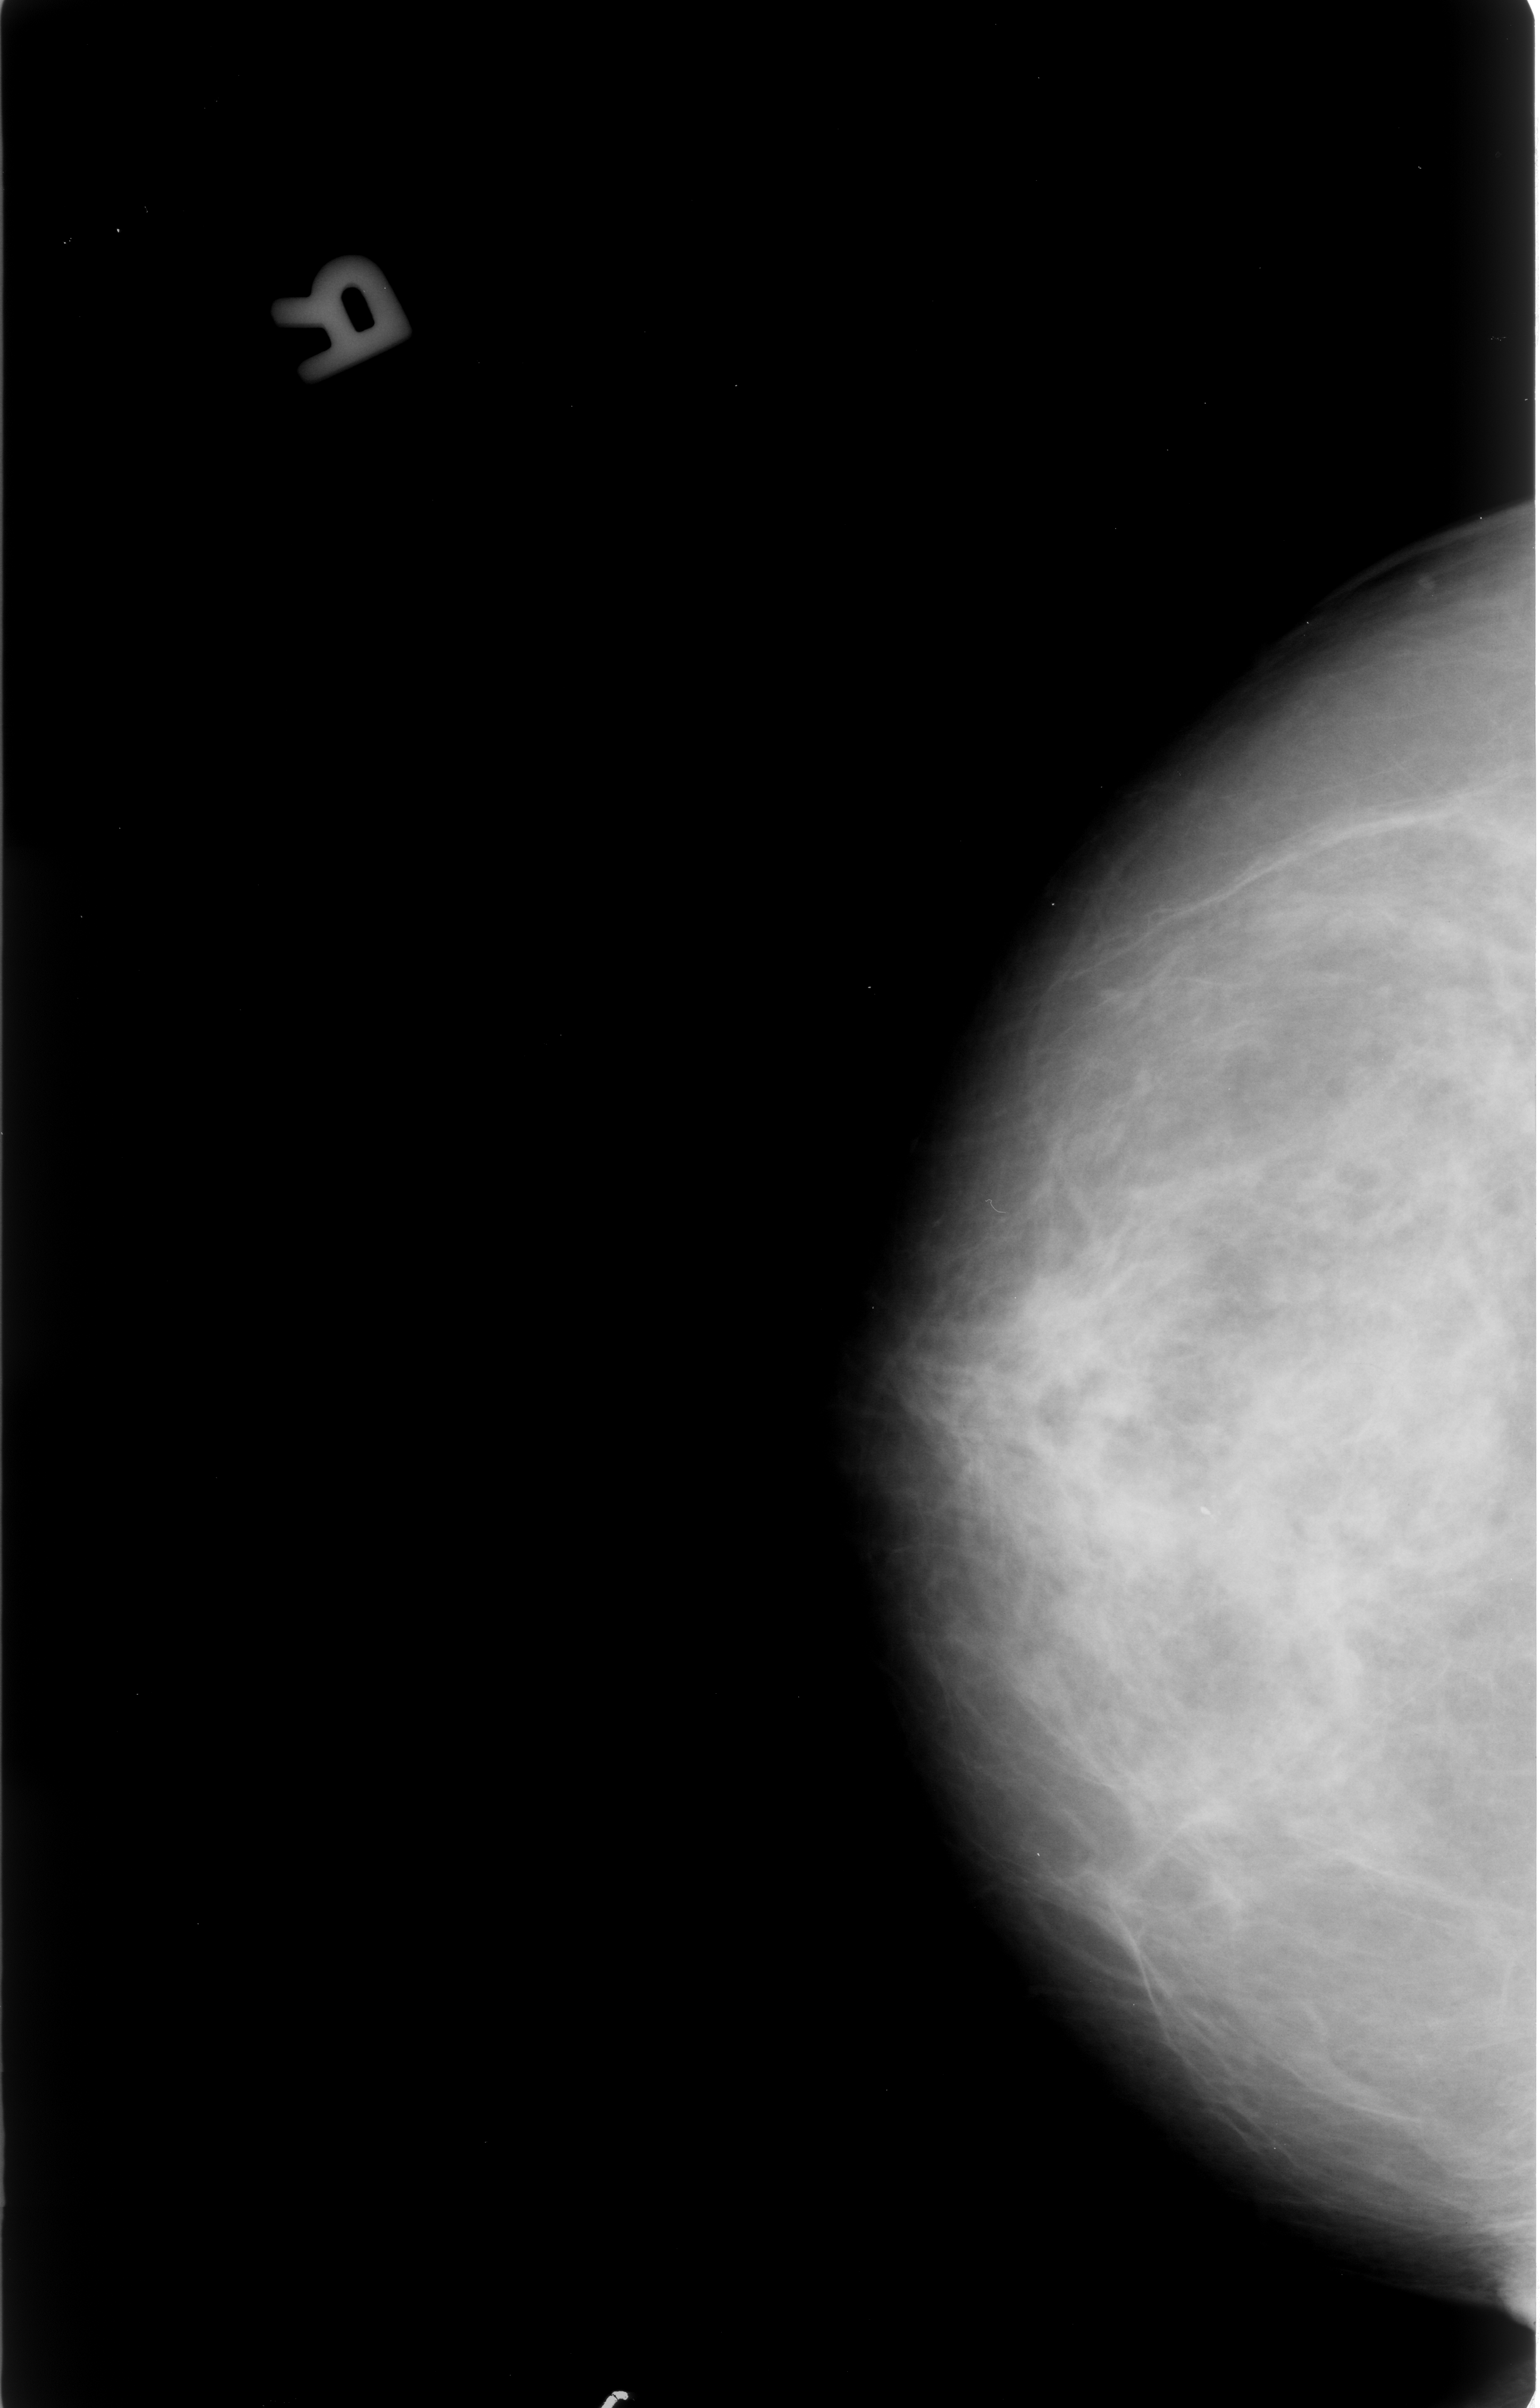
Scanned film-screen mammogram. Right breast. Craniocaudal (CC) view. BI-RADS breast density category 2 (scale 1–4). 1540 × 2408 image matrix.
Marked abnormalities (boxes around the expert regions of interest):
- calcifications, morphology punctate, distribution clustered; BI-RADS assessment category 3; pathology (as recorded): malignant: bounding box (x1, y1, x2, y2) in pixels: (965, 1250, 1396, 1584)